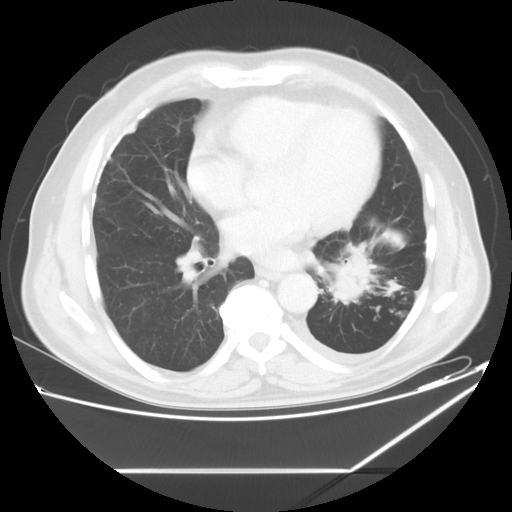
Chest CT, one axial slice; slice 26 of 60 in the series (ordered by position); reconstruction kernel STANDARD; 120 kVp; lung window (W 1500 / L -600 HU); 5 mm slice thickness; 512 × 512 image matrix. Male patient, age 62 years. Case-level facts recorded for this patient, not image findings: clinical TNM (as recorded): T3 N0 M1.
Annotated regions visible in this slice (rectangle marked by the reading radiologist):
- lung tumour (recorded histology: adenocarcinoma): box from (x=324, y=242) to (x=384, y=318) px
- lung tumour (recorded histology: adenocarcinoma): (x=331, y=243)–(x=378, y=303)